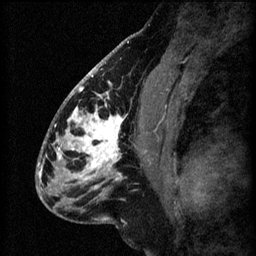
Breast MRI (dynamic contrast-enhanced), one sagittal slice; position 32 of 60 along the scan axis; 3 images stored at this slice position (order not interpretable as contrast timing); 1.5 T; TE 4.2 ms, TR 8.2 ms; 2.2 mm slice thickness; 256 × 256 image matrix. Patient: female, 41 years.
Structures marked on this image (semi-automatic segmentation, software-assisted and operator-edited):
- analysis volume of interest (the breast-tissue region the enhancement analysis was run in; not a lesion): bounding box (x1, y1, x2, y2) in pixels: (56, 104, 157, 207)
- tumour enhancement mask (voxels above the 70 % enhancement threshold inside the analysis volume of interest): (56, 104, 147, 197)